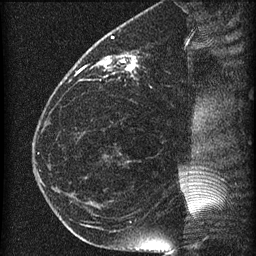
Breast MRI (dynamic contrast-enhanced), one sagittal slice. Slice 23 of 60 in the series (ordered by position). Dynamic contrast-enhanced series, image 2 of 4 at this slice position (ordered by acquisition). 1.5 T. TE 4.2 ms, TR 22.7 ms. 1.5 mm slice thickness. 256 × 256 image matrix, field of view 180 × 180 mm. Patient: female, 35 years. Case-level facts recorded for this patient, not image findings: setting: breast cancer imaged before/during neoadjuvant chemotherapy; receptor status: HR-positive, HER2-negative.
Annotated regions visible in this slice (semi-automatic segmentation, software-assisted and operator-edited):
- analysis volume of interest (the breast-tissue region the enhancement analysis was run in; not a lesion): bounding box <69,27,199,112> (left, top, right, bottom; pixels)
- tumour enhancement mask (voxels above the 90 % enhancement threshold inside the analysis volume of interest): <77,54,136,77>